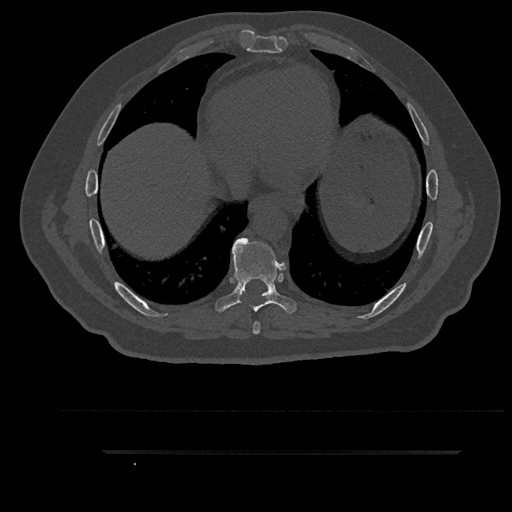
CT including the spine, one axial slice. Slice 481 of 797 in the series (ordered by position). Reconstruction kernel Br40s/3. 120 kVp. Bone window (W 1800 / L 400 HU). 0.5 mm slice thickness. 512 × 512 image matrix. Patient: male, 63 years. Case-level facts recorded for this patient, not image findings: primary cancer: renal; vertebrae with lytic lesions (as recorded): T8.
Annotated regions visible in this slice (semi-automatic segmentation, software-assisted and operator-edited):
- T7 vertebra: box from (x=253, y=321) to (x=260, y=334) px
- T8 vertebra: (x=215, y=238)–(x=297, y=315)